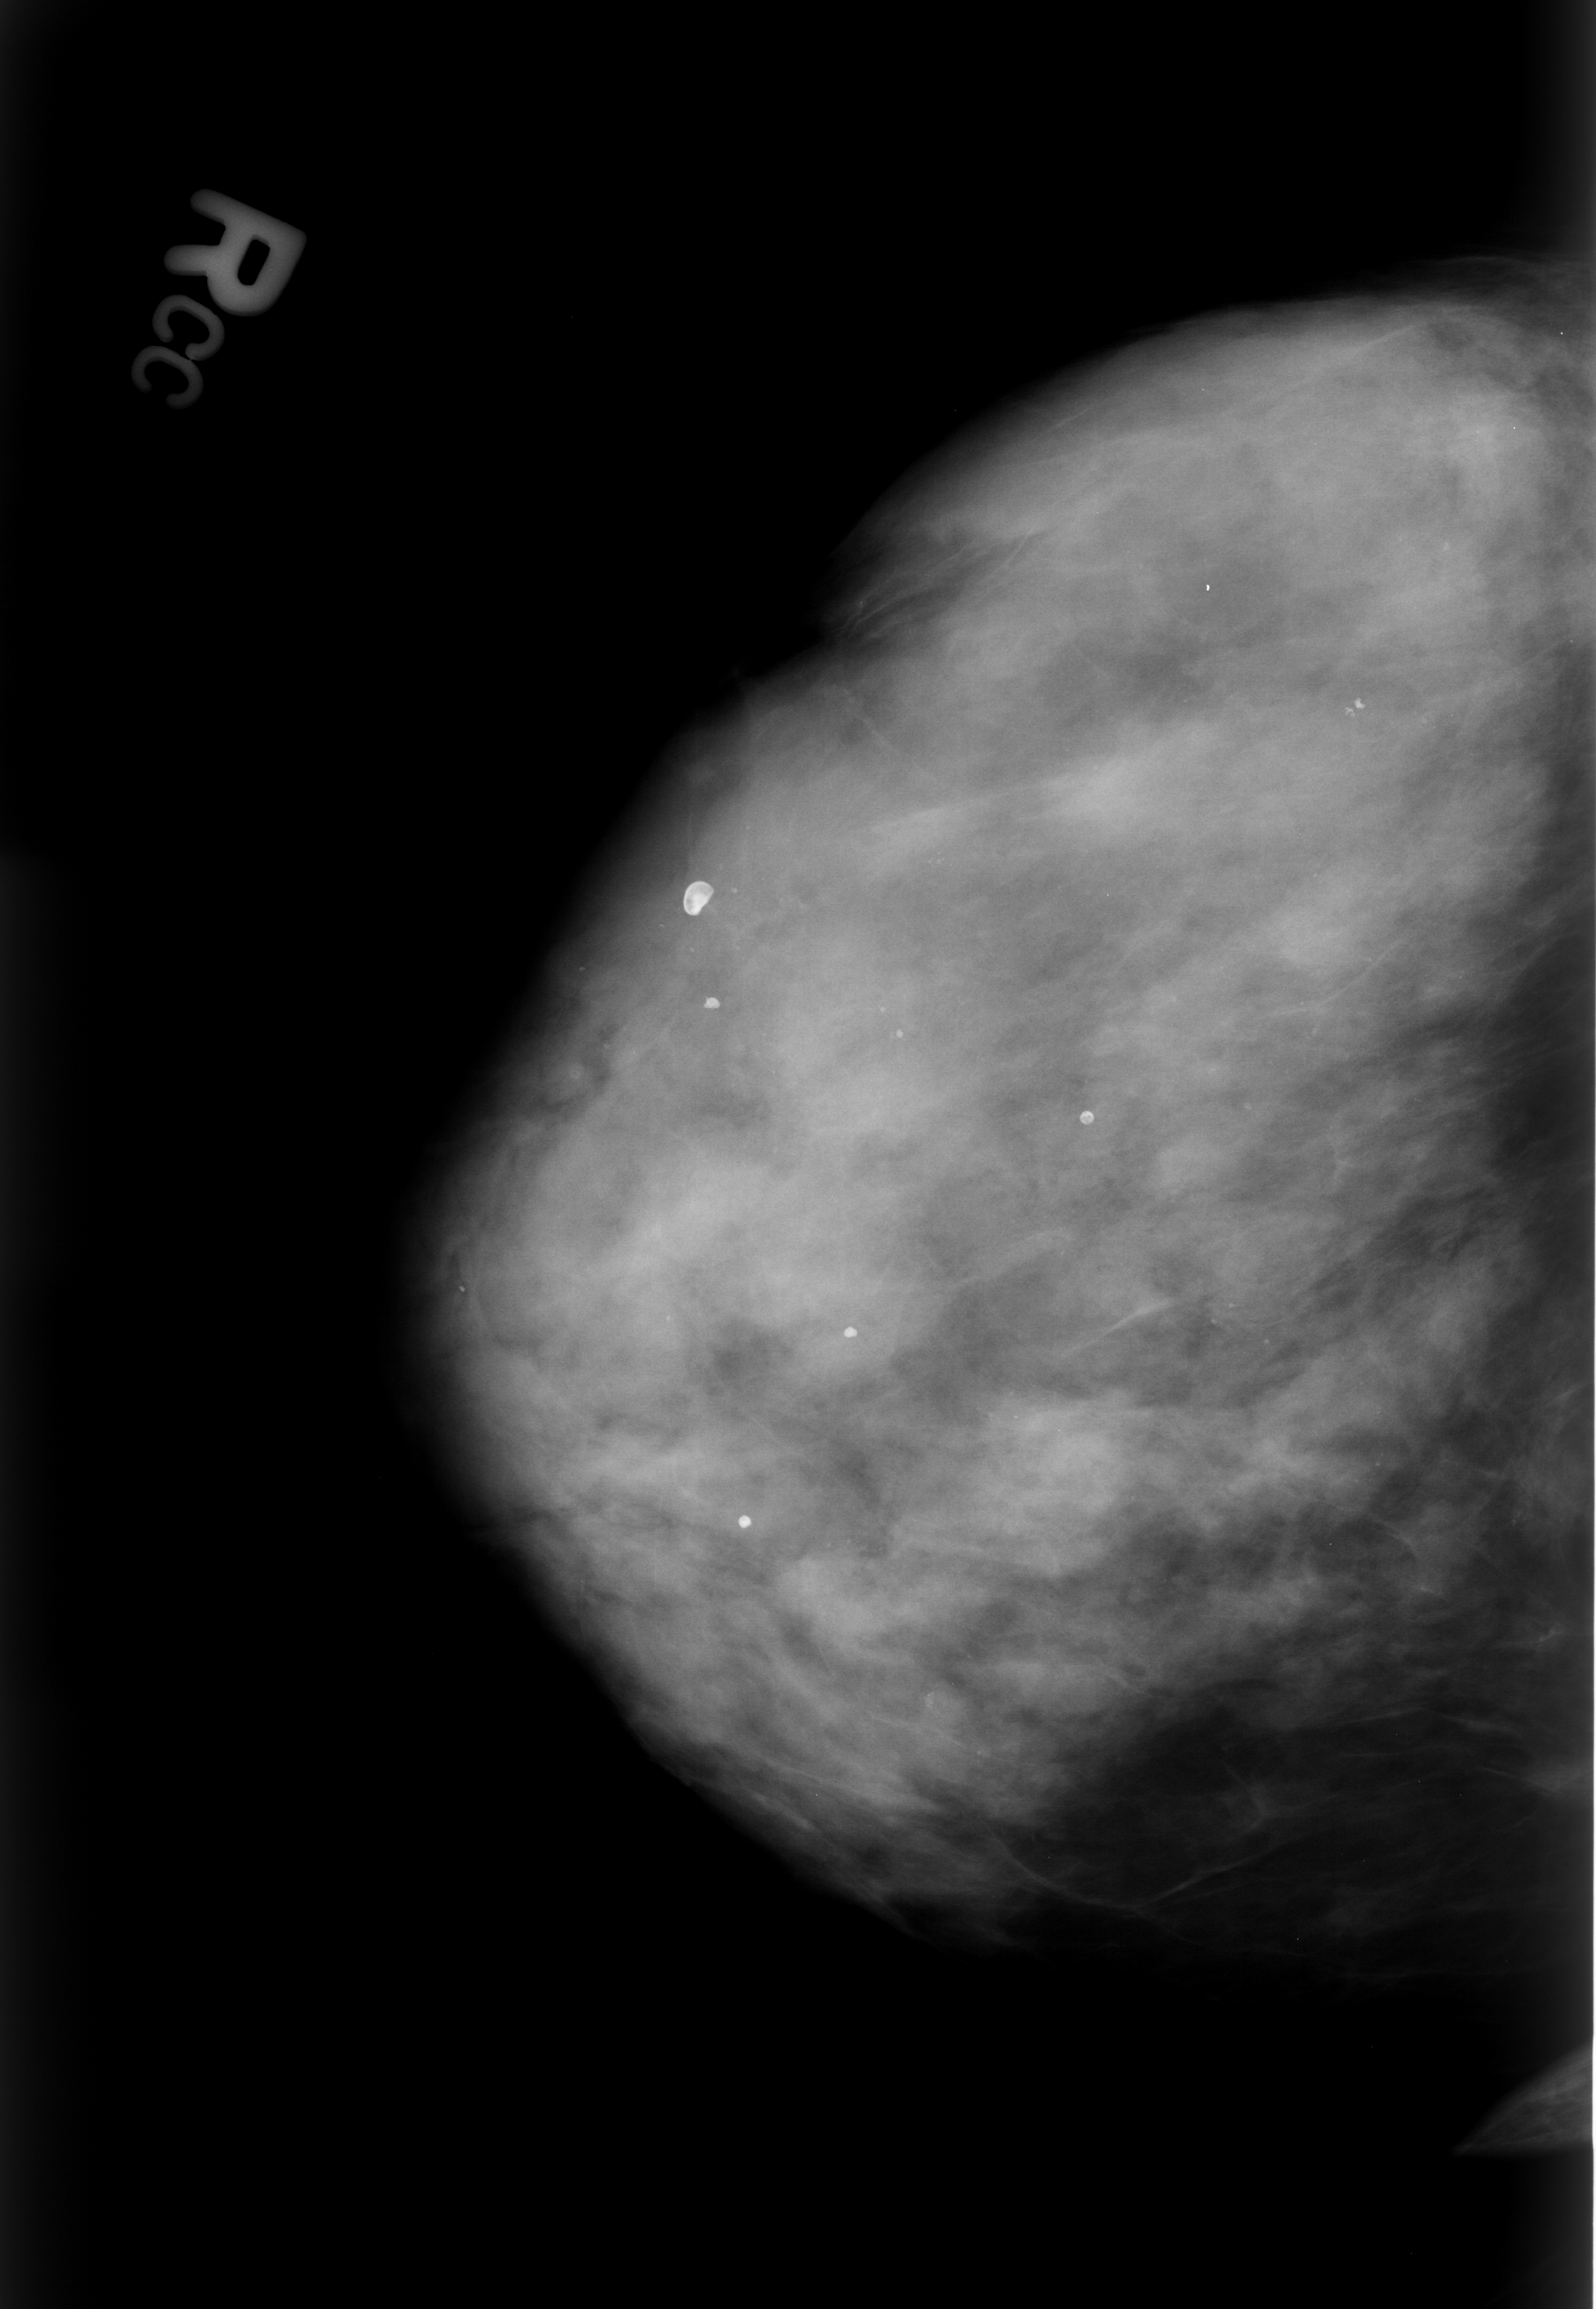
Mammogram (digitized film); right breast; craniocaudal (CC) view; BI-RADS breast density category 4 (scale 1–4).
Abnormality record for this image: Finding 1 of 6: calcifications, morphology round and regular / lucent center / punctate, distribution diffusely scattered; BI-RADS assessment category 2; benign without callback (not worked up further). Finding 2 of 6: calcifications, morphology round and regular / lucent center / punctate, distribution diffusely scattered; BI-RADS assessment category 2; benign without callback (not worked up further). Finding 3 of 6: calcifications, morphology round and regular / lucent center / punctate, distribution diffusely scattered; BI-RADS assessment category 2; benign without callback (not worked up further). Finding 4 of 6: calcifications, morphology round and regular / lucent center / punctate, distribution diffusely scattered; BI-RADS assessment category 2; subtlety rating 5 on a 1 (subtle) to 5 (obvious) scale; benign; no additional work-up was recommended (benign without callback). Finding 5 of 6: calcifications, morphology round and regular / lucent center / punctate, distribution diffusely scattered; BI-RADS assessment category 2; benign; no additional work-up was recommended (benign without callback). Finding 6 of 6: calcifications, morphology round and regular / lucent center / punctate, distribution diffusely scattered; BI-RADS assessment category 2; subtlety rating 5 on a 1 (subtle) to 5 (obvious) scale; benign without callback (not worked up further).